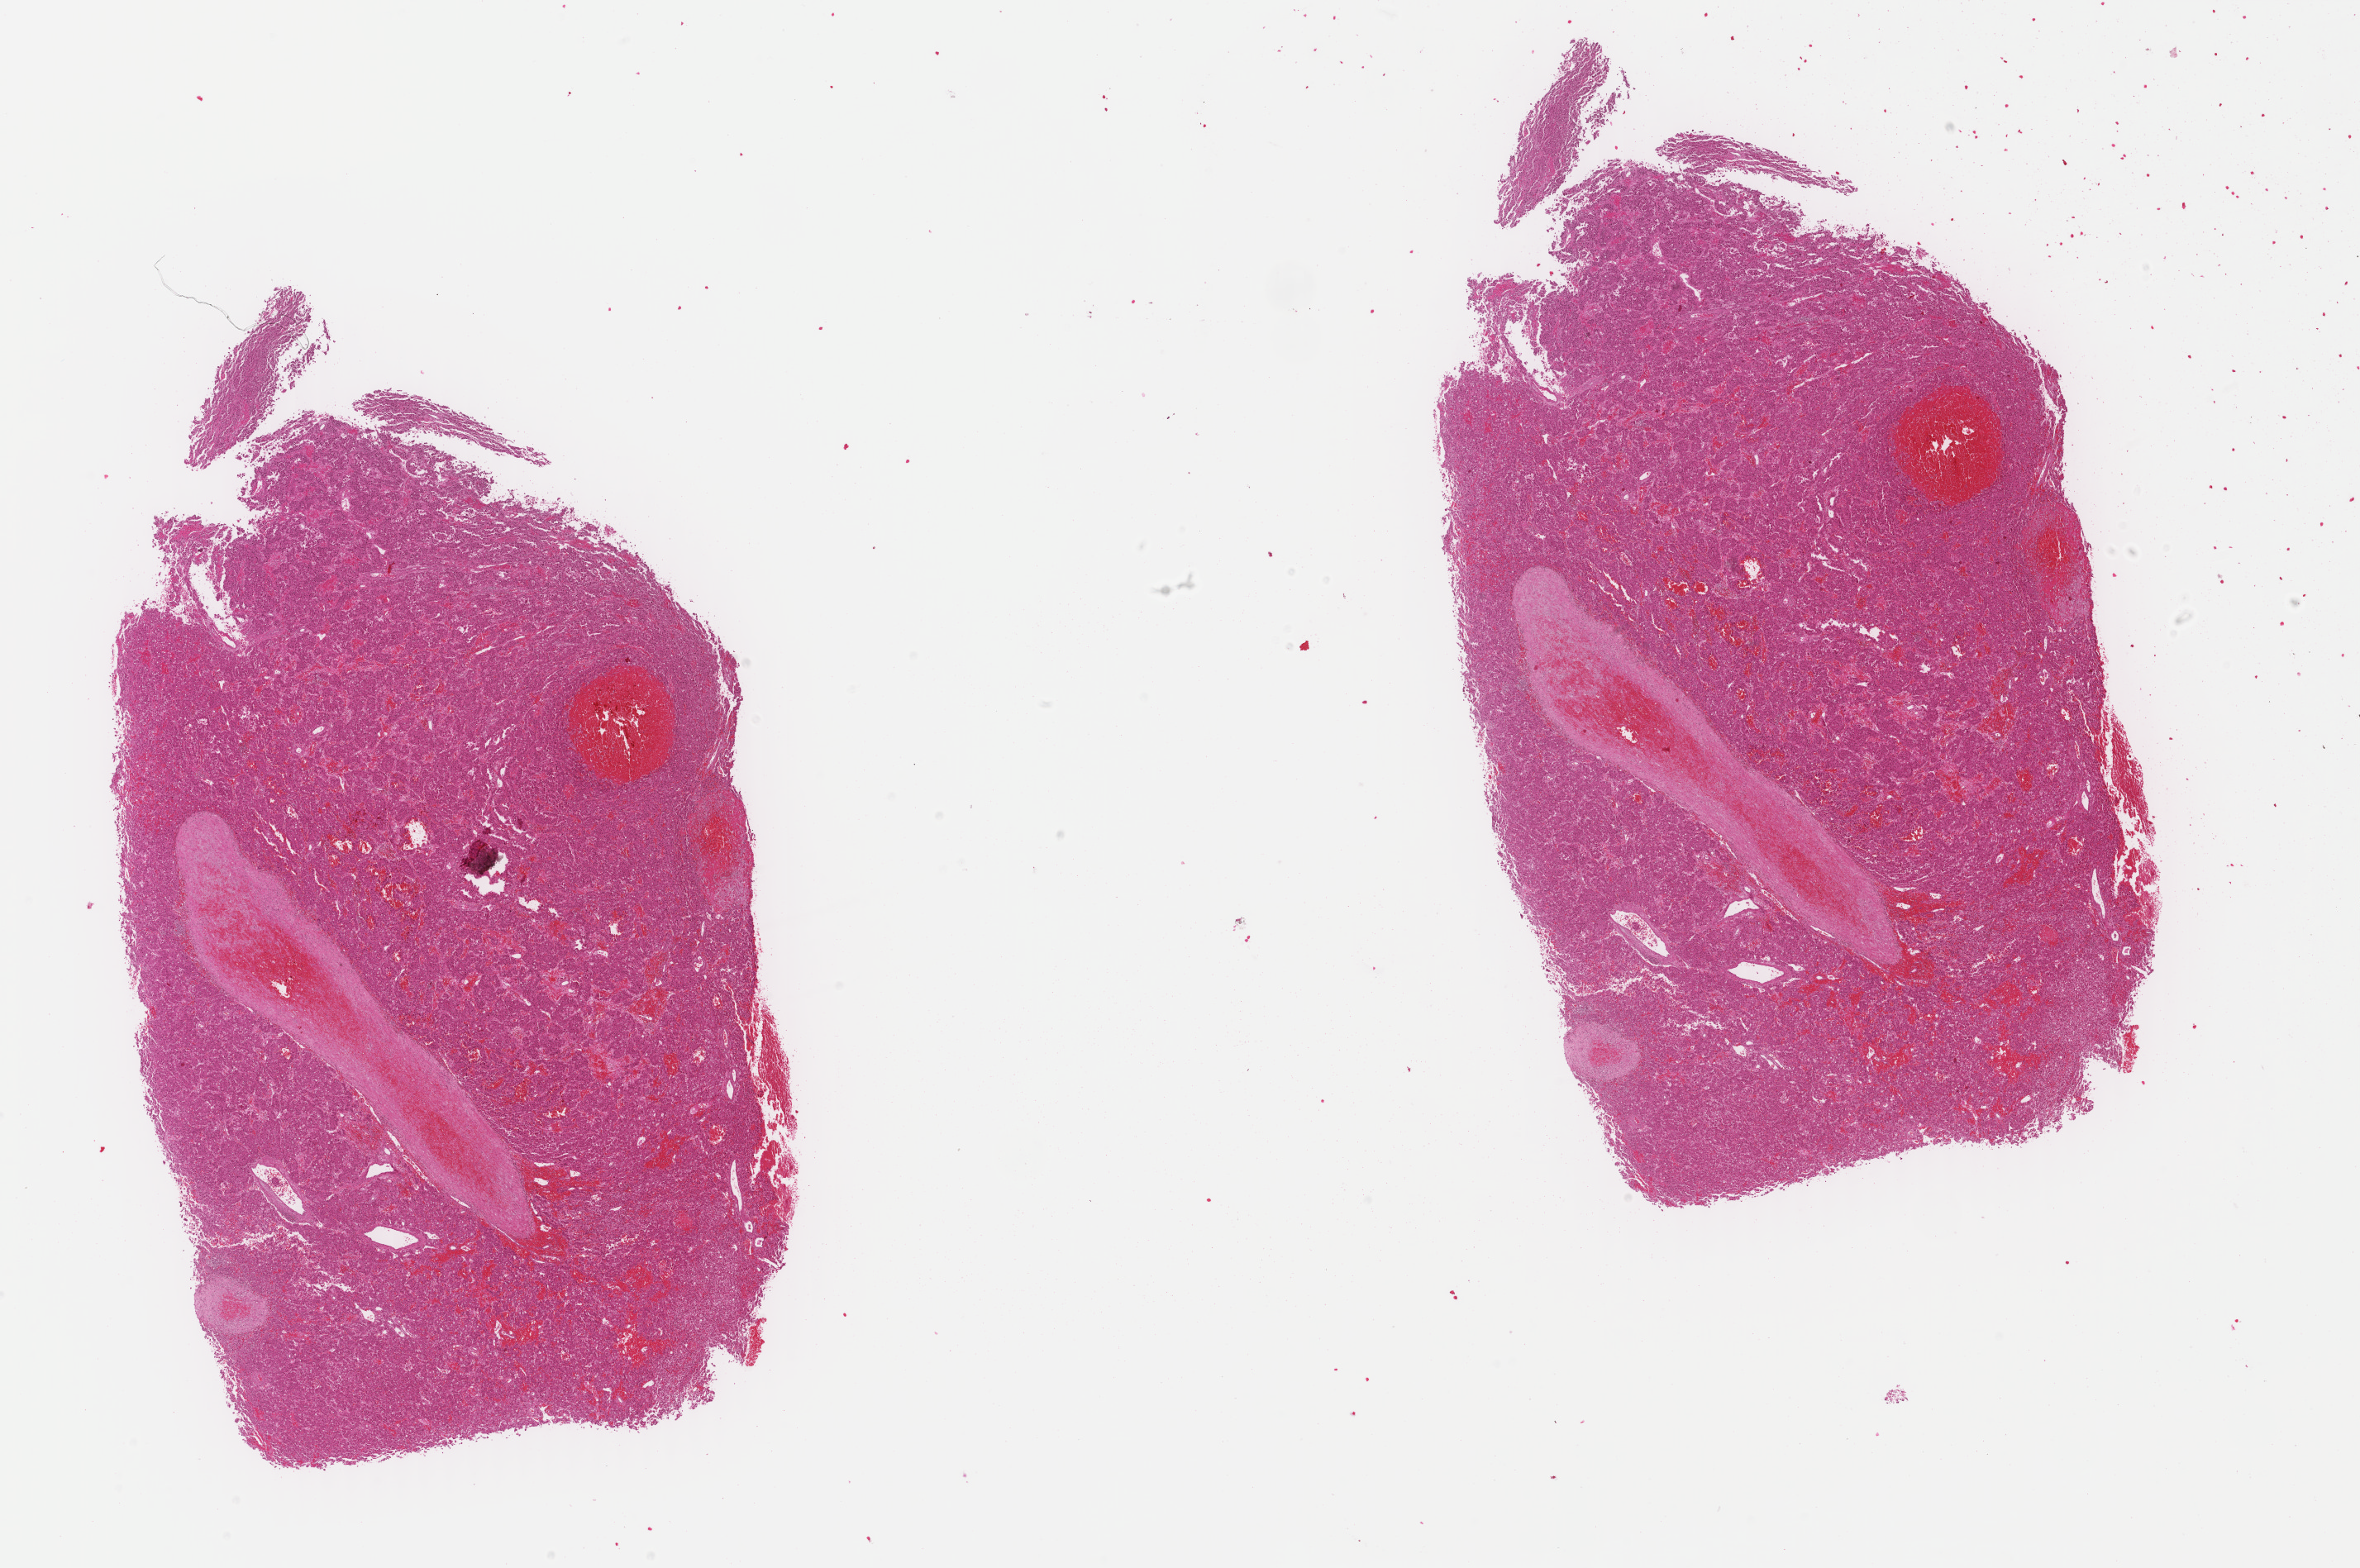
Whole-slide histology image, H&E-stained, whole scanned area (about 22.7 x 15.1 mm) shown as a low-resolution overview; formalin-fixed paraffin-embedded (FFPE) diagnostic section; sample: primary tumour, liver. Patient: female, age at initial diagnosis 51 years. Histologic grade: G1 (well differentiated).
• histologic diagnosis: Hepatocellular carcinoma, NOS